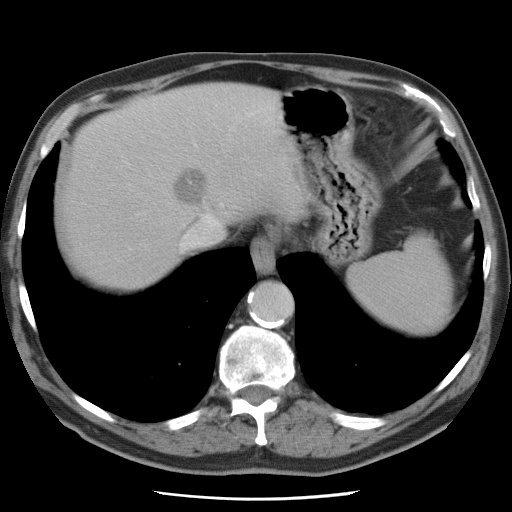
Contrast-enhanced abdominal CT, one axial slice; position 66 of 78 along the scan axis; intravenous contrast given; soft-tissue window (W 400 / L 40 HU); 5 mm slice thickness; 512 × 512 image matrix, field of view 337 × 337 mm. Male patient, age 75 years. From the clinical record (not read from this slice): diagnosis: colorectal cancer liver metastases, imaged before liver resection; multiple liver metastases: yes; largest metastasis: 2.4 cm.
Annotated regions visible in this slice (expert manual segmentation):
- hepatic veins: box from (x=179, y=116) to (x=240, y=252) px
- liver: (x=64, y=84)–(x=300, y=290)
- planned liver remnant (the part of the liver to remain after resection): (x=64, y=141)–(x=180, y=291)
- liver metastasis: (x=173, y=168)–(x=209, y=207)